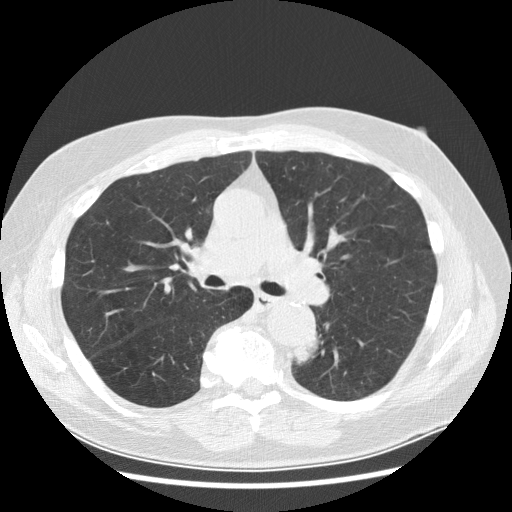
Low-dose screening chest CT, one axial slice. Slice 173 of 282 in the series (ordered by position). Reconstruction kernel STANDARD. 120 kVp. Lung window (W 1500 / L -600 HU). 2.5 mm slice thickness. 512 × 512 image matrix, field of view 370 × 370 mm.
Structures marked on this image (manually delineated by an expert):
- lesion 1 (tumor, lower lobe of left lung): bounding box <294,343,318,365> (left, top, right, bottom; pixels)